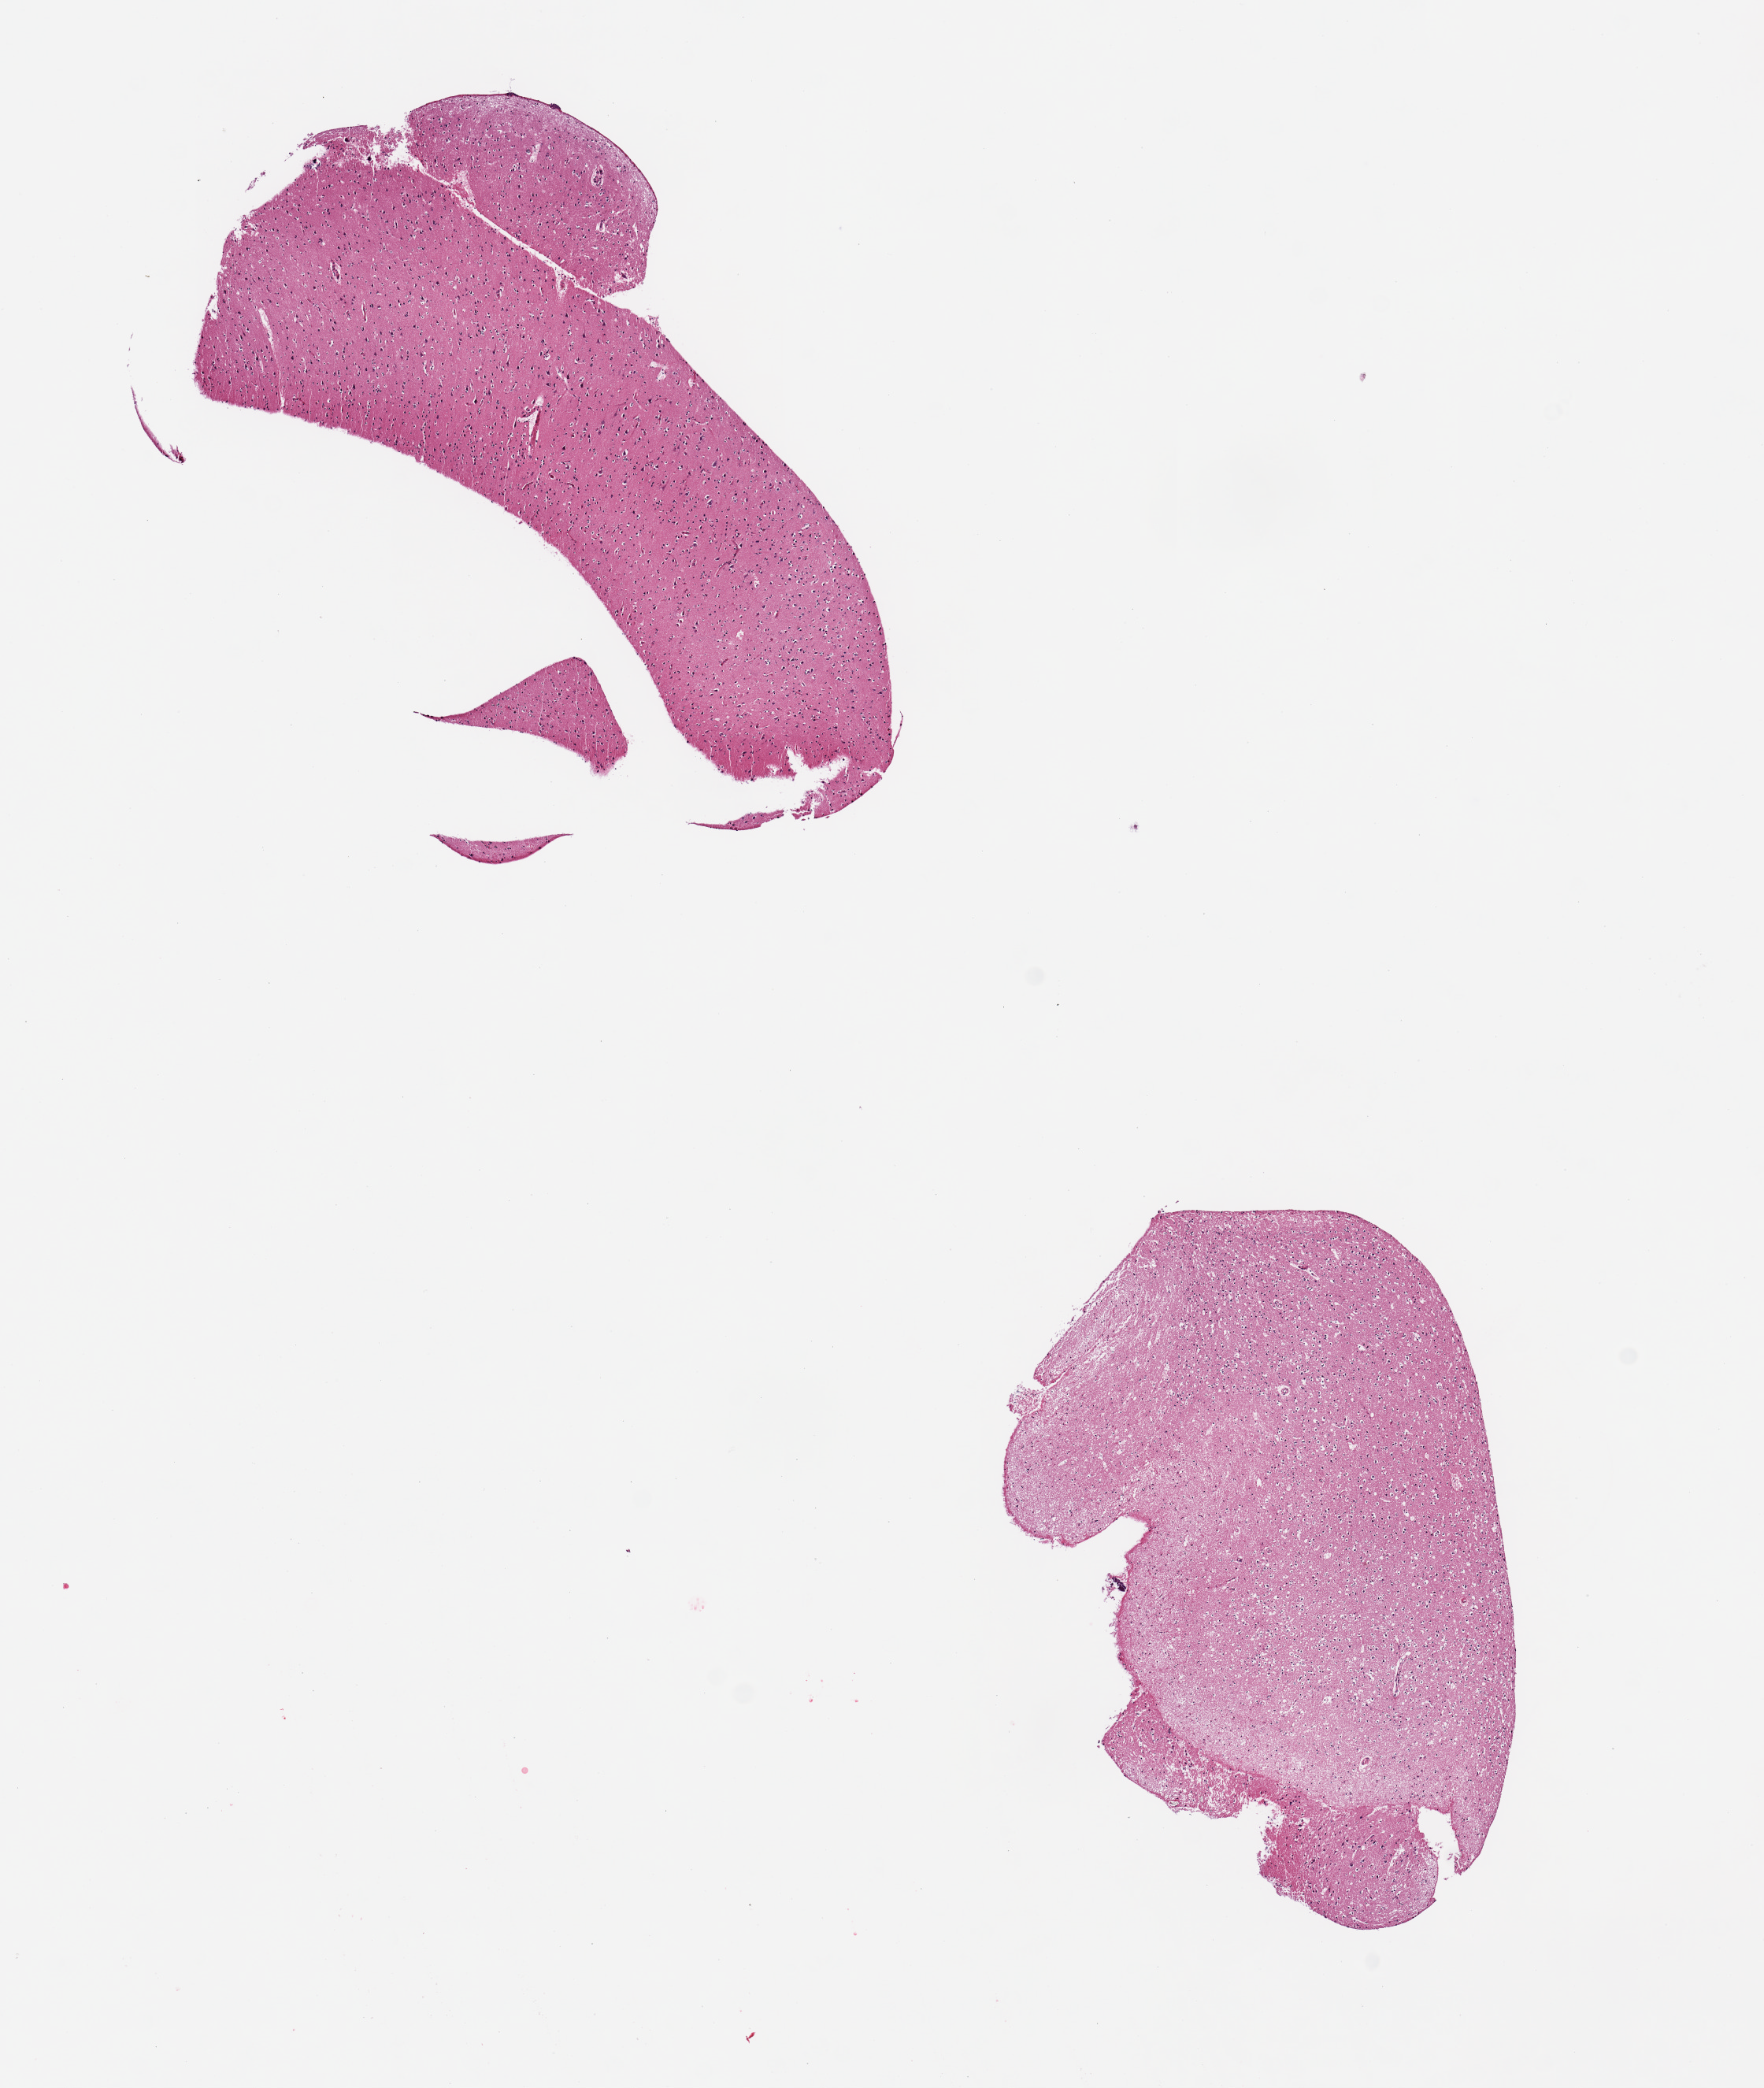
Digitized H&E-stained section — a low-resolution overview of the entire scanned area, about 8.9 x 10.5 mm. PAXgene-fixed, paraffin-embedded tissue. Section of cerebral cortex (target tissue). Tissue donor sample. Female donor.
* pathologist's review note for this sample: 2 pieces; one appears better preserved than the other